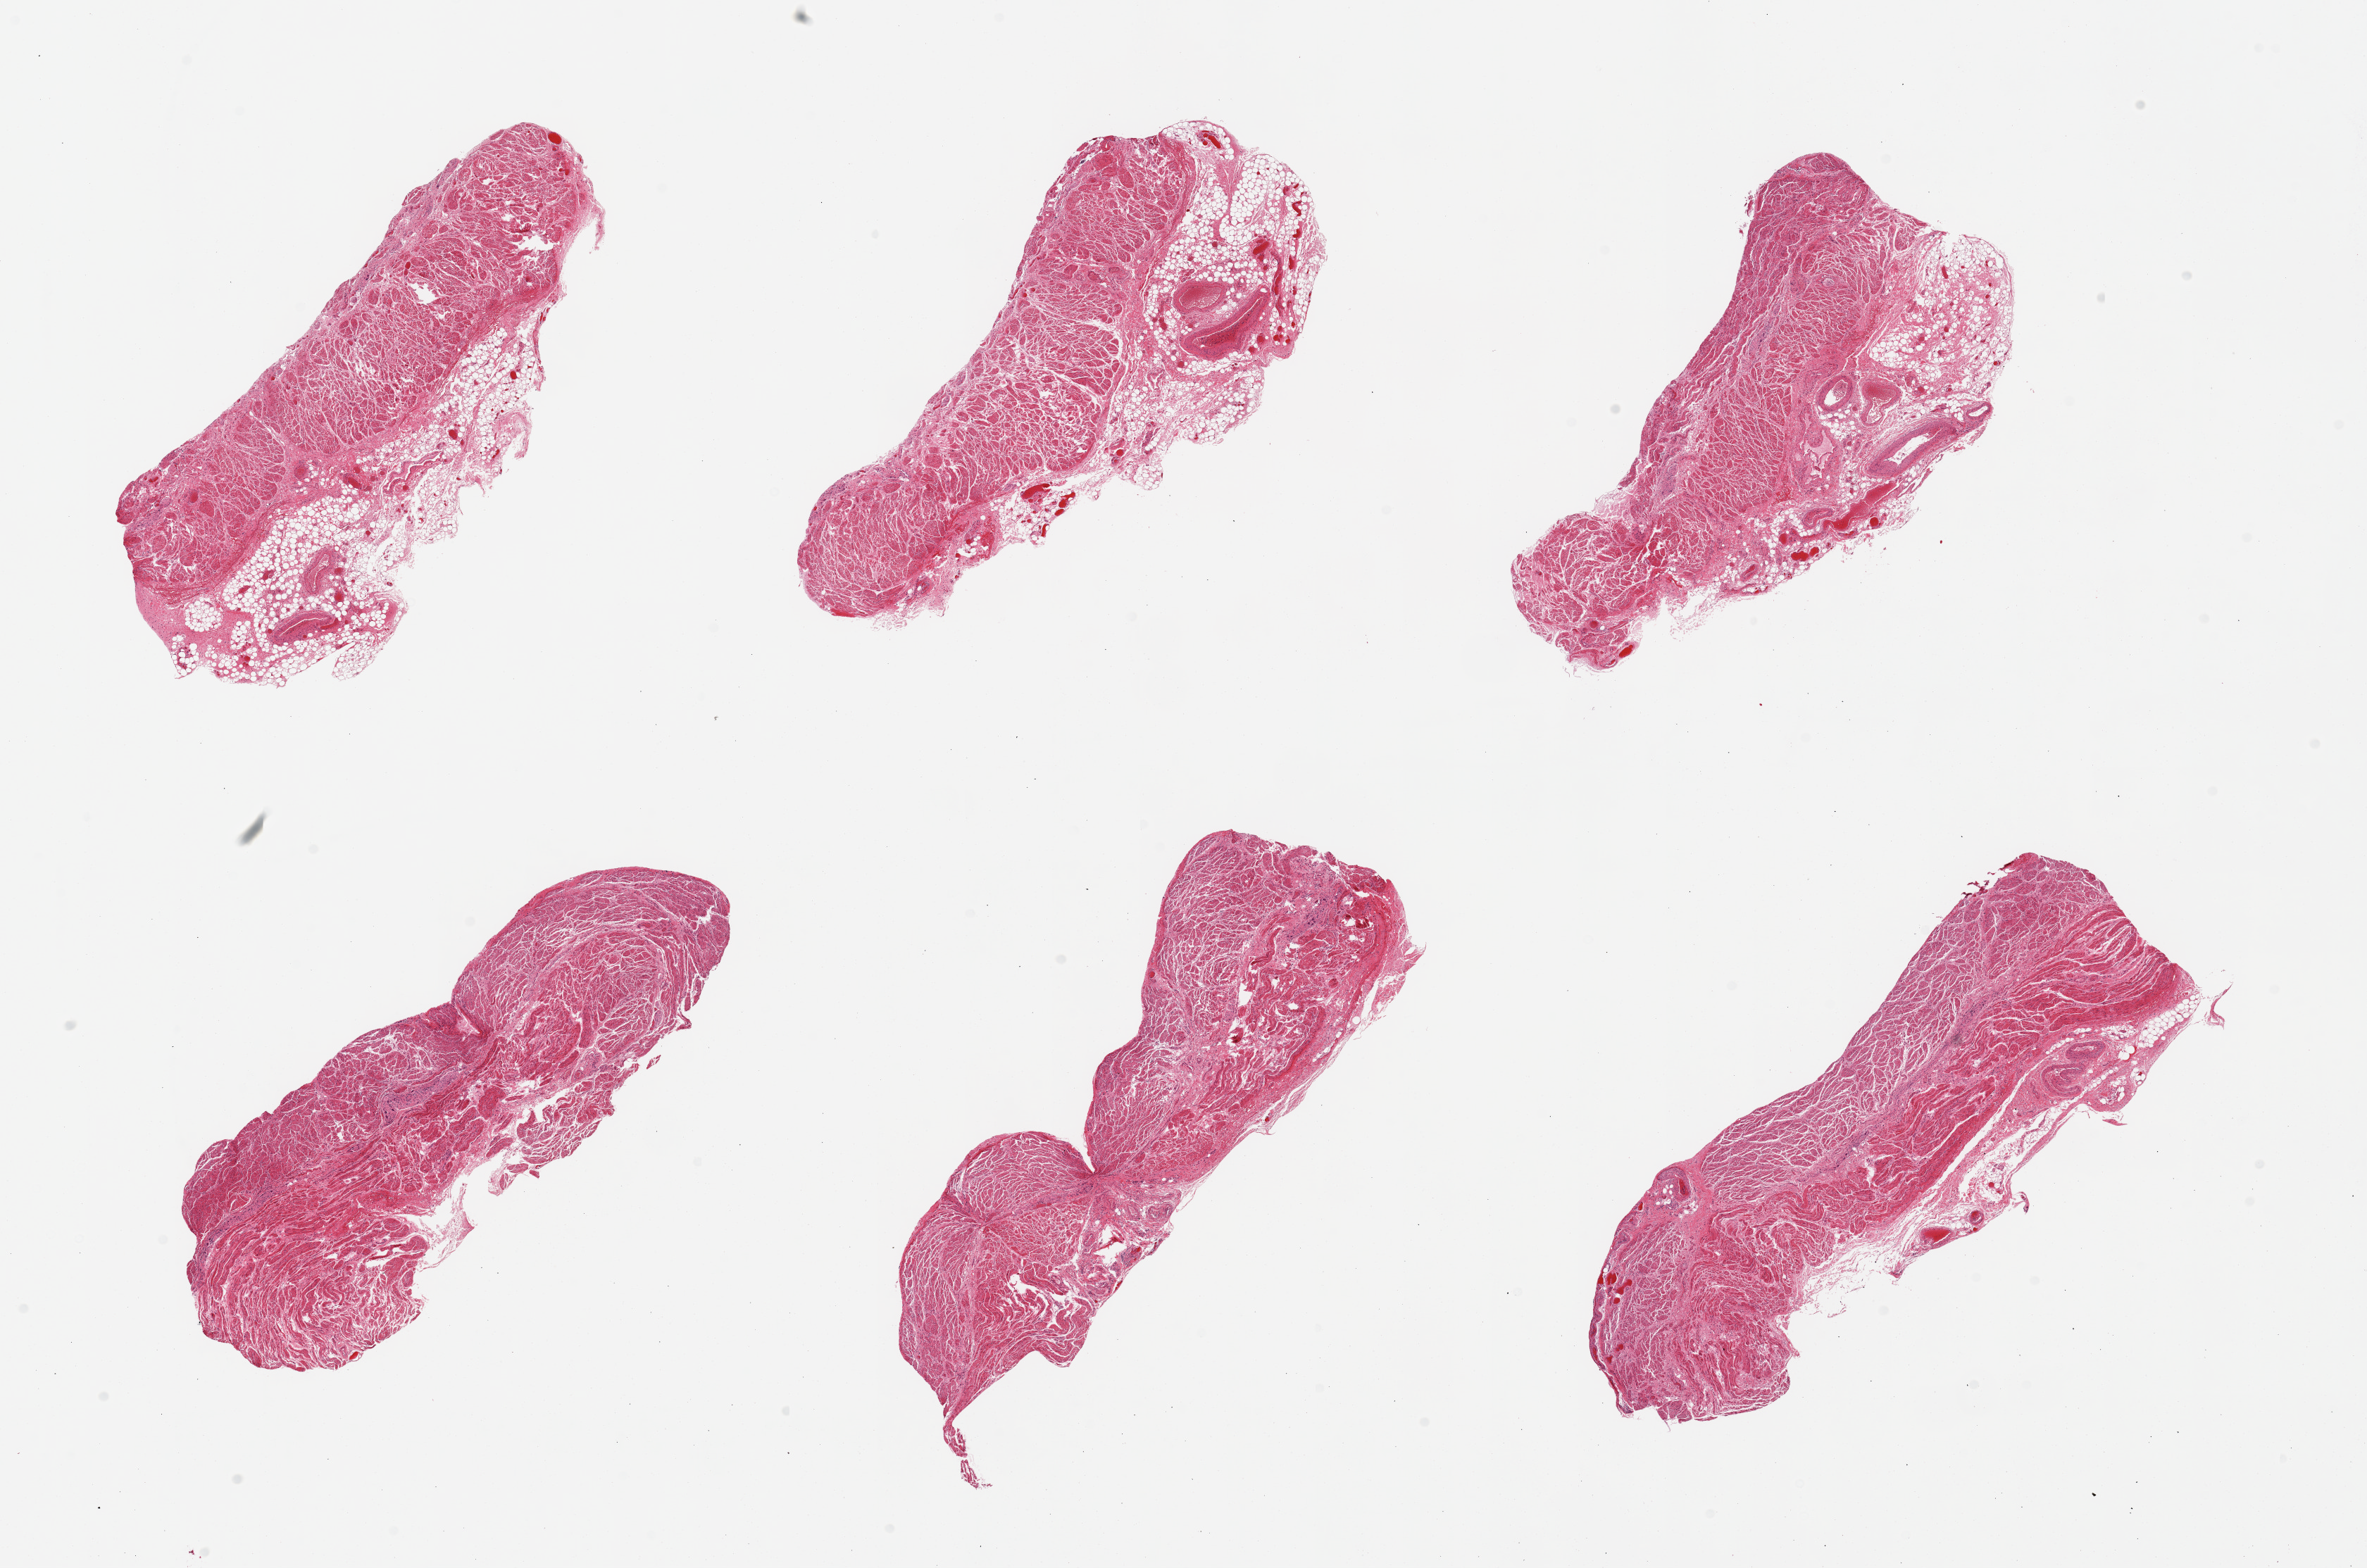
Digitized H&E-stained section, whole scanned area (about 26.6 x 17.6 mm) shown as a low-resolution overview, PAXgene-fixed paraffin-embedded (PFPE) section, section of gastroesophageal junction (target tissue), tissue donor sample. Male donor.
Review note (as recorded): 6 pieces, adherent fat/serosa on several sections up to ~1.5mm.